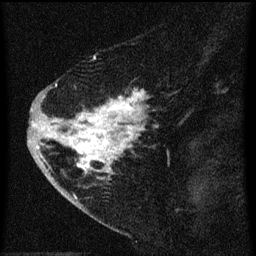
Breast MRI (dynamic contrast-enhanced), one sagittal slice. Position 20 of 60 along the scan axis. Dynamic contrast-enhanced series, image 2 of 3 at this slice position (ordered by acquisition). 1.5 T. TE 4.2 ms, TR 8 ms. 2 mm slice thickness. 256 × 256 image matrix, field of view 180 × 180 mm. Female patient, age 47 years.
Annotated regions visible in this slice (semi-automatically segmented with operator editing):
- analysis volume of interest (the breast-tissue region the enhancement analysis was run in; not a lesion): bounding box [x1, y1, x2, y2] px = [38, 76, 158, 193]
- tumour enhancement mask (voxels above the 70 % enhancement threshold inside the analysis volume of interest): [38, 84, 158, 179]